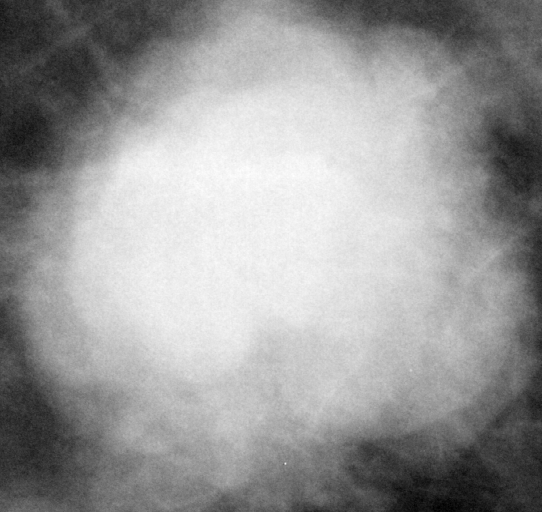
Region of interest cut from a scanned film mammogram (one marked finding), right breast, CC view.
Mass, shape lobulated, margins microlobulated; BI-RADS assessment category 5; pathology result (as recorded, not read from the image): malignant.